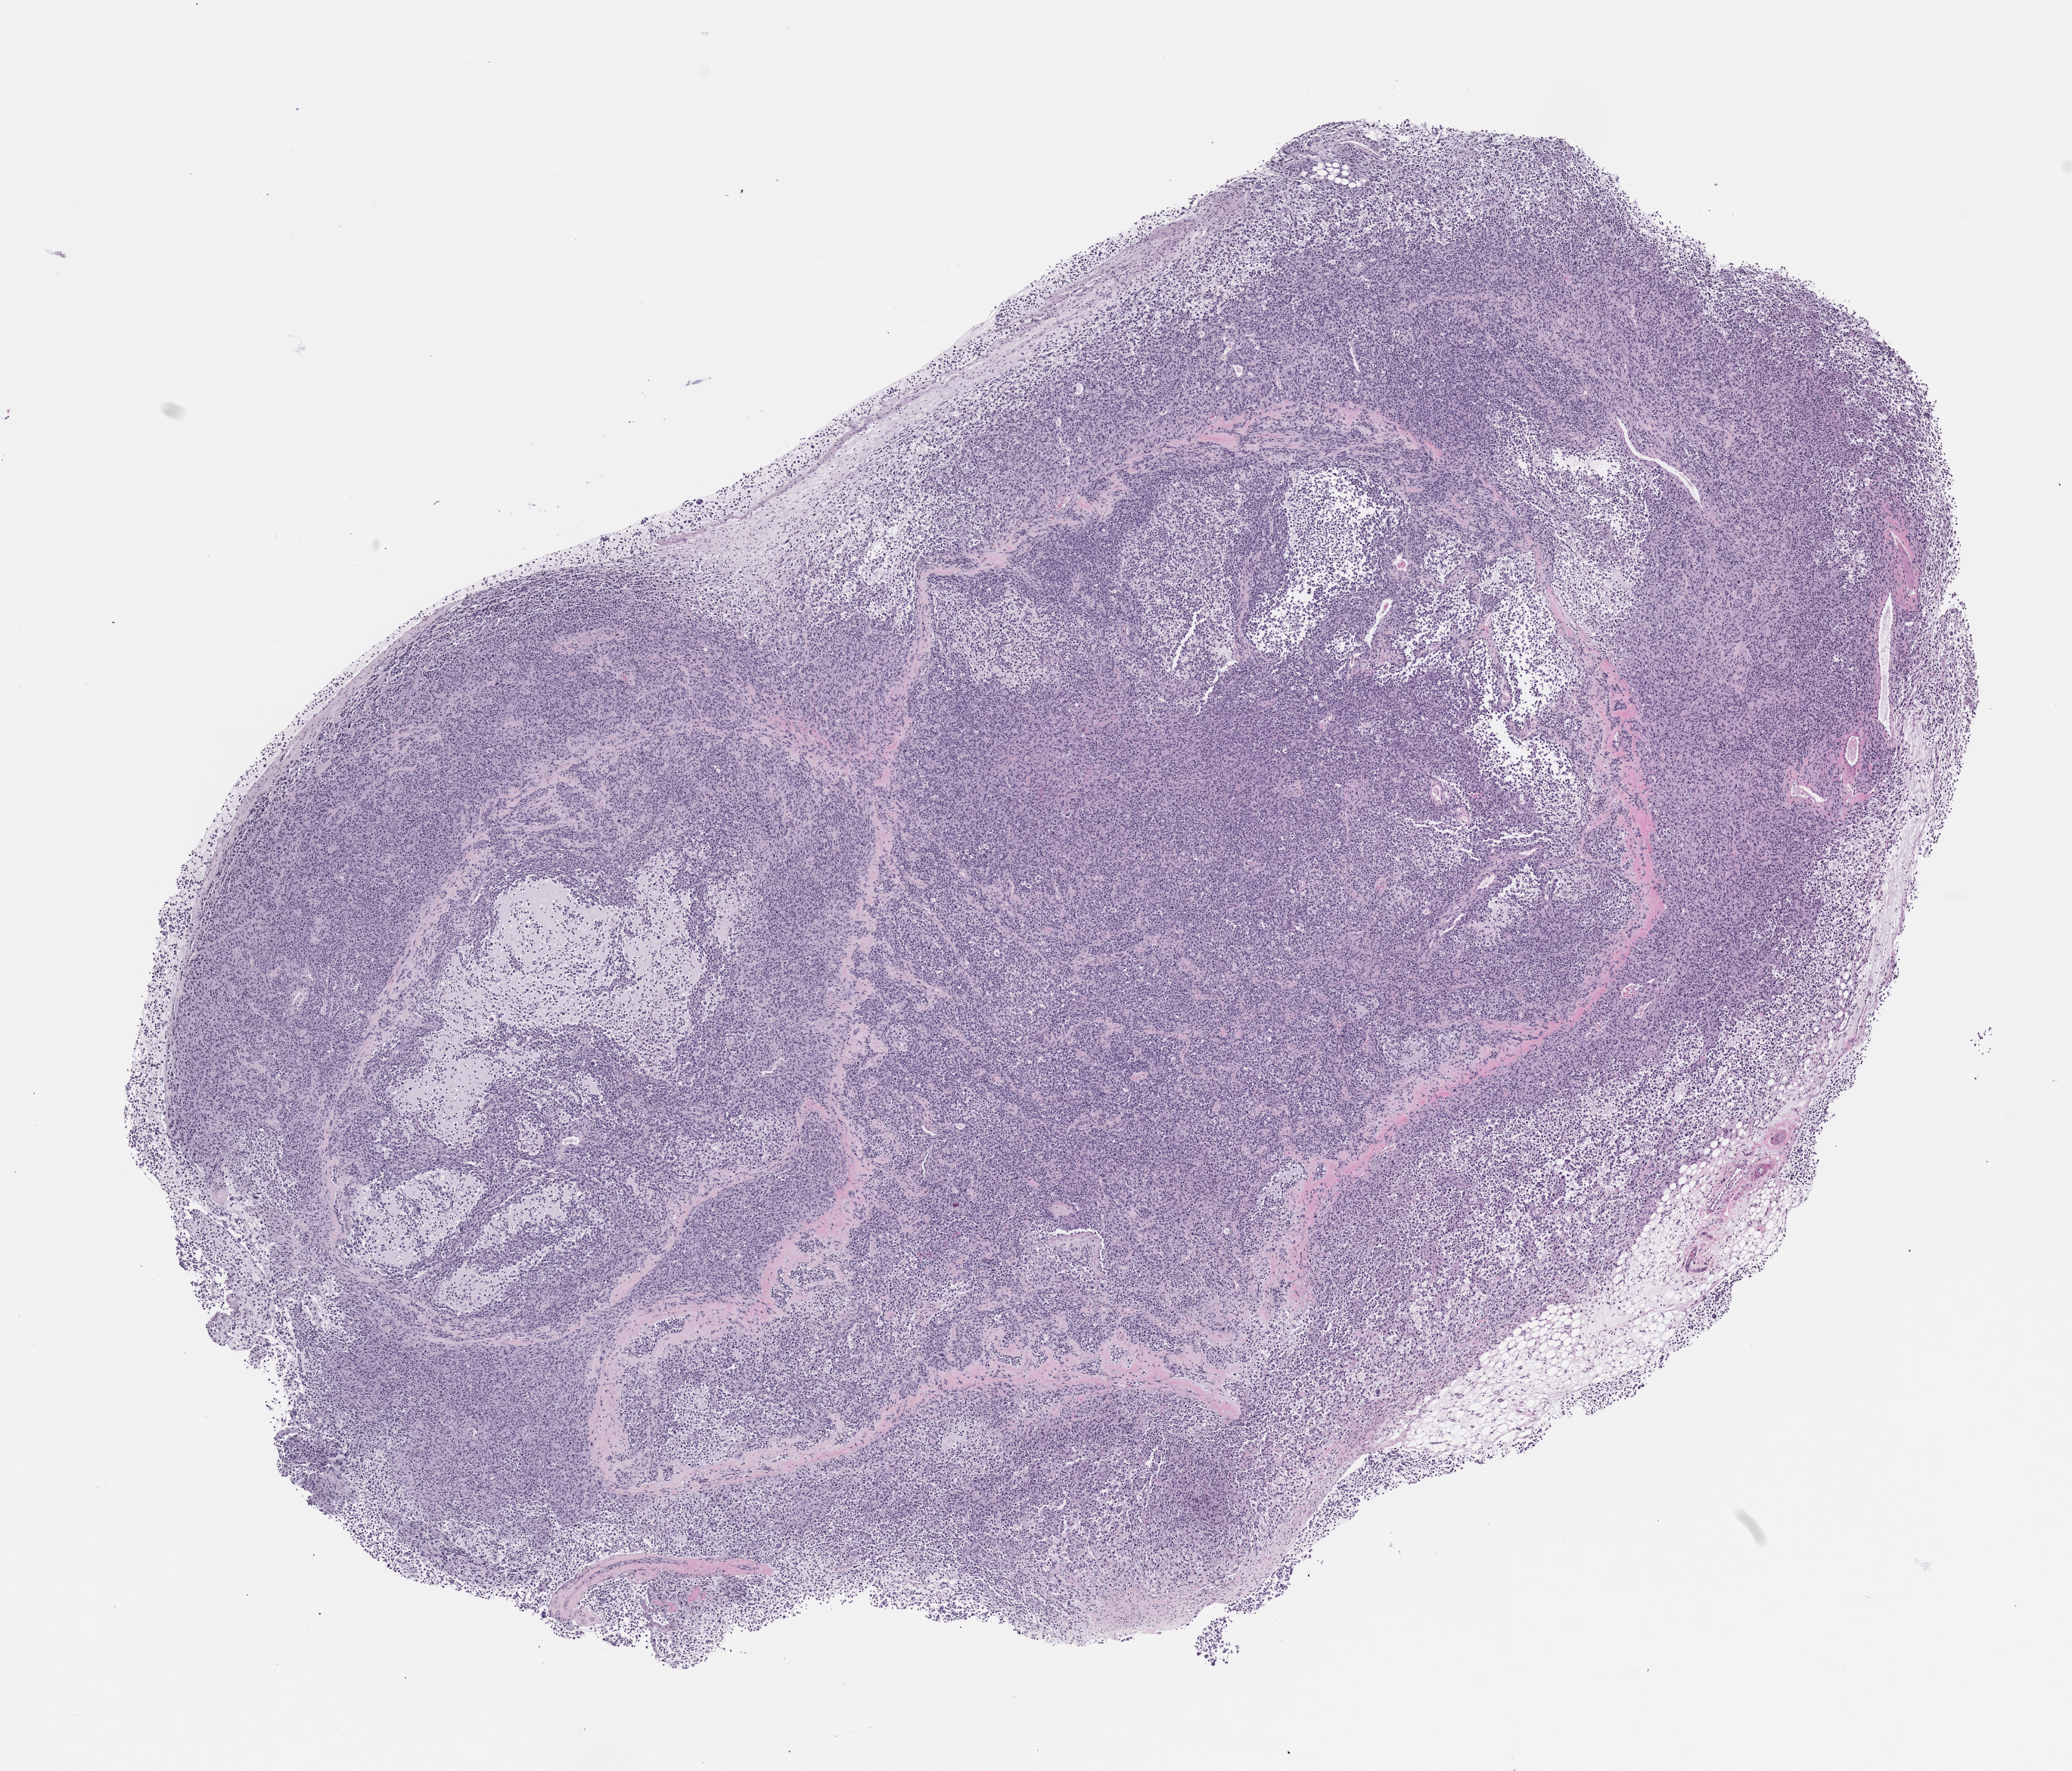
H&E whole-slide image of a patient-derived xenograft (PDX) tumor grown in a mouse, passage 1 — shown as a low-resolution overview of the whole scanned area (about 11.0 x 9.4 mm), FFPE section, tumor site category: musculoskeletal.
Originating patient diagnosis: Rhabdomyosarcoma.